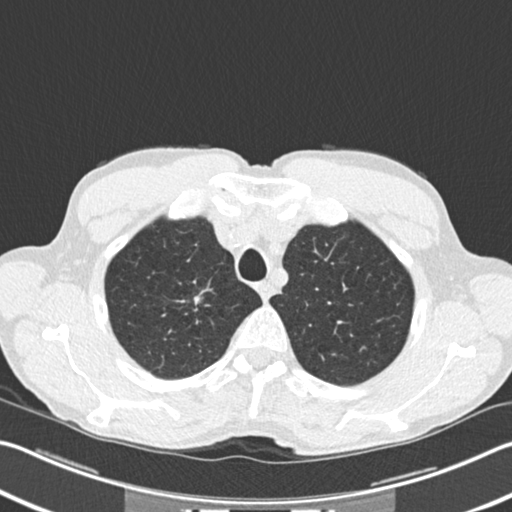
Low-dose screening chest CT, one axial slice; reconstruction kernel B30f; lung window (W 1500 / L -600 HU); 2 mm slice thickness; 512 × 512 image matrix, field of view 342 × 342 mm.
Outlined on this slice (expert manual segmentation):
- lesion 1 (tumor, upper lobe of right lung): bounding box (x1, y1, x2, y2) in pixels: (194, 295, 201, 304)